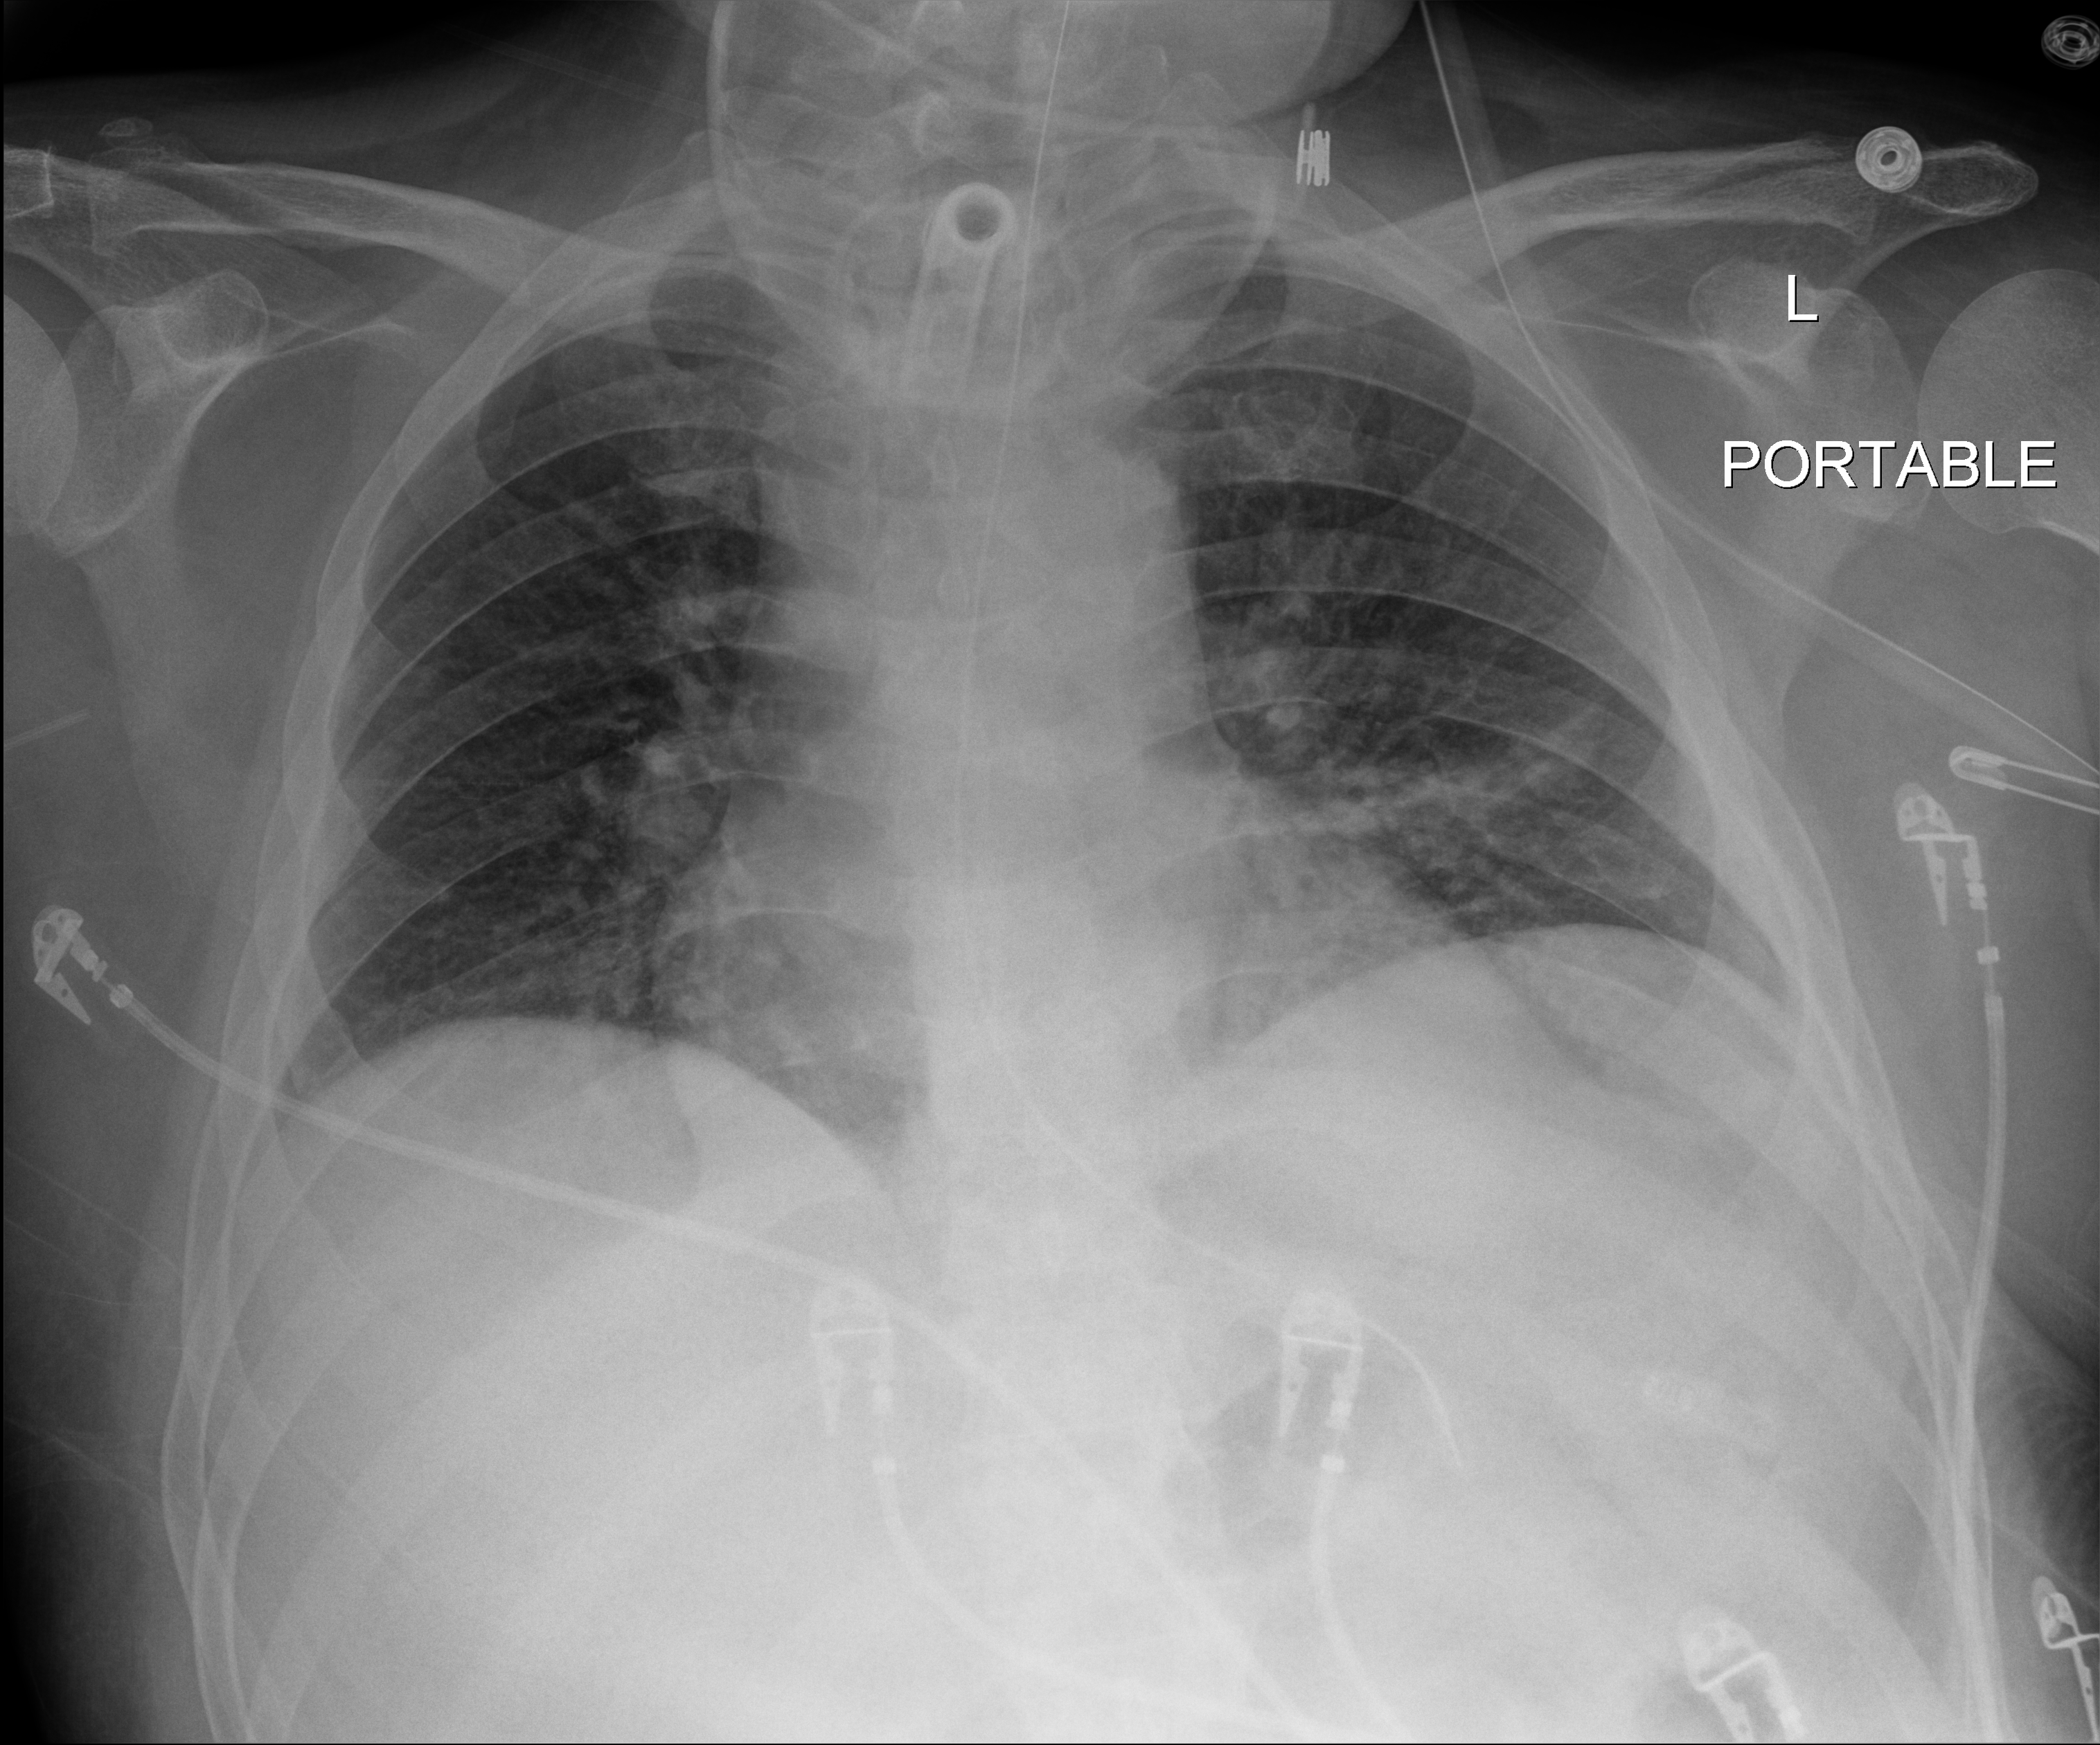
Bedside chest radiograph (digital radiography); anteroposterior (AP) projection. Male patient hospitalised with COVID-19, age 18–59 years.
Hospital-stay facts (about this admission, not read from this image; timing relative to this image not recorded): mechanically ventilated during this hospital stay: yes; admitted to intensive care during this hospital stay: yes; length of hospital stay: 65 days.